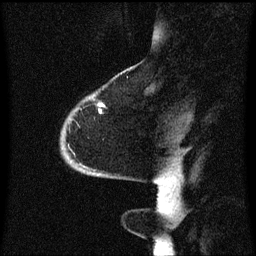
Breast MRI (dynamic contrast-enhanced), one sagittal slice; slice 13 of 60 in the series (ordered by position); dynamic contrast-enhanced series, image 2 of 3 at this slice position (ordered by acquisition); 1.5 T; TE 4.2 ms, TR 8.4 ms; 2 mm slice thickness; 256 × 256 image matrix. Female patient, age 68 years. From the clinical record (not read from this slice): setting: breast cancer imaged before/during neoadjuvant chemotherapy; receptor status: triple-negative.
Structures marked on this image (semi-automatic segmentation, software-assisted and operator-edited):
- analysis volume of interest (the breast-tissue region the enhancement analysis was run in; not a lesion): bounding box <62,94,106,173> (left, top, right, bottom; pixels)
- tumour enhancement mask (voxels above the 70 % enhancement threshold inside the analysis volume of interest): <99,106,105,113>